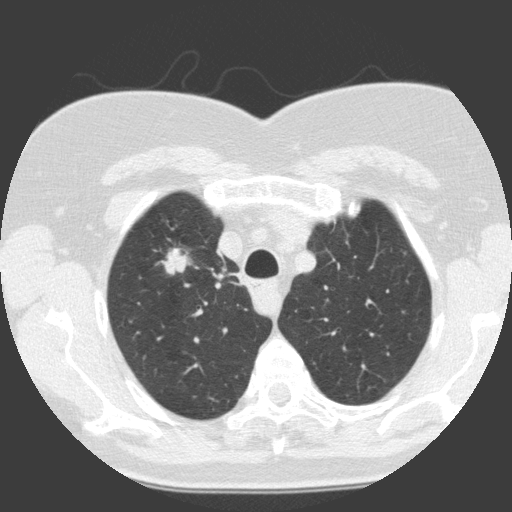
Axial slice from a low-dose chest CT screening exam; baseline annual screen; lung window (W 1500 / L -600 HU); 2 mm slice thickness; standard (soft-tissue) reconstruction kernel (C); slice 29 of 146 in the series. Female participant, aged 68 years at enrolment. Current smoker at enrolment.
- Expert reader's lesion annotation, bounding box <154,243,199,286> (left, top, right, bottom; pixels).
- Screening reader's record for this exam (one nodule recorded; not confirmed to be the boxed lesion): non-calcified nodule or mass ≥4 mm, right upper lobe, 19 × 12 mm, smooth margins, soft tissue attenuation.